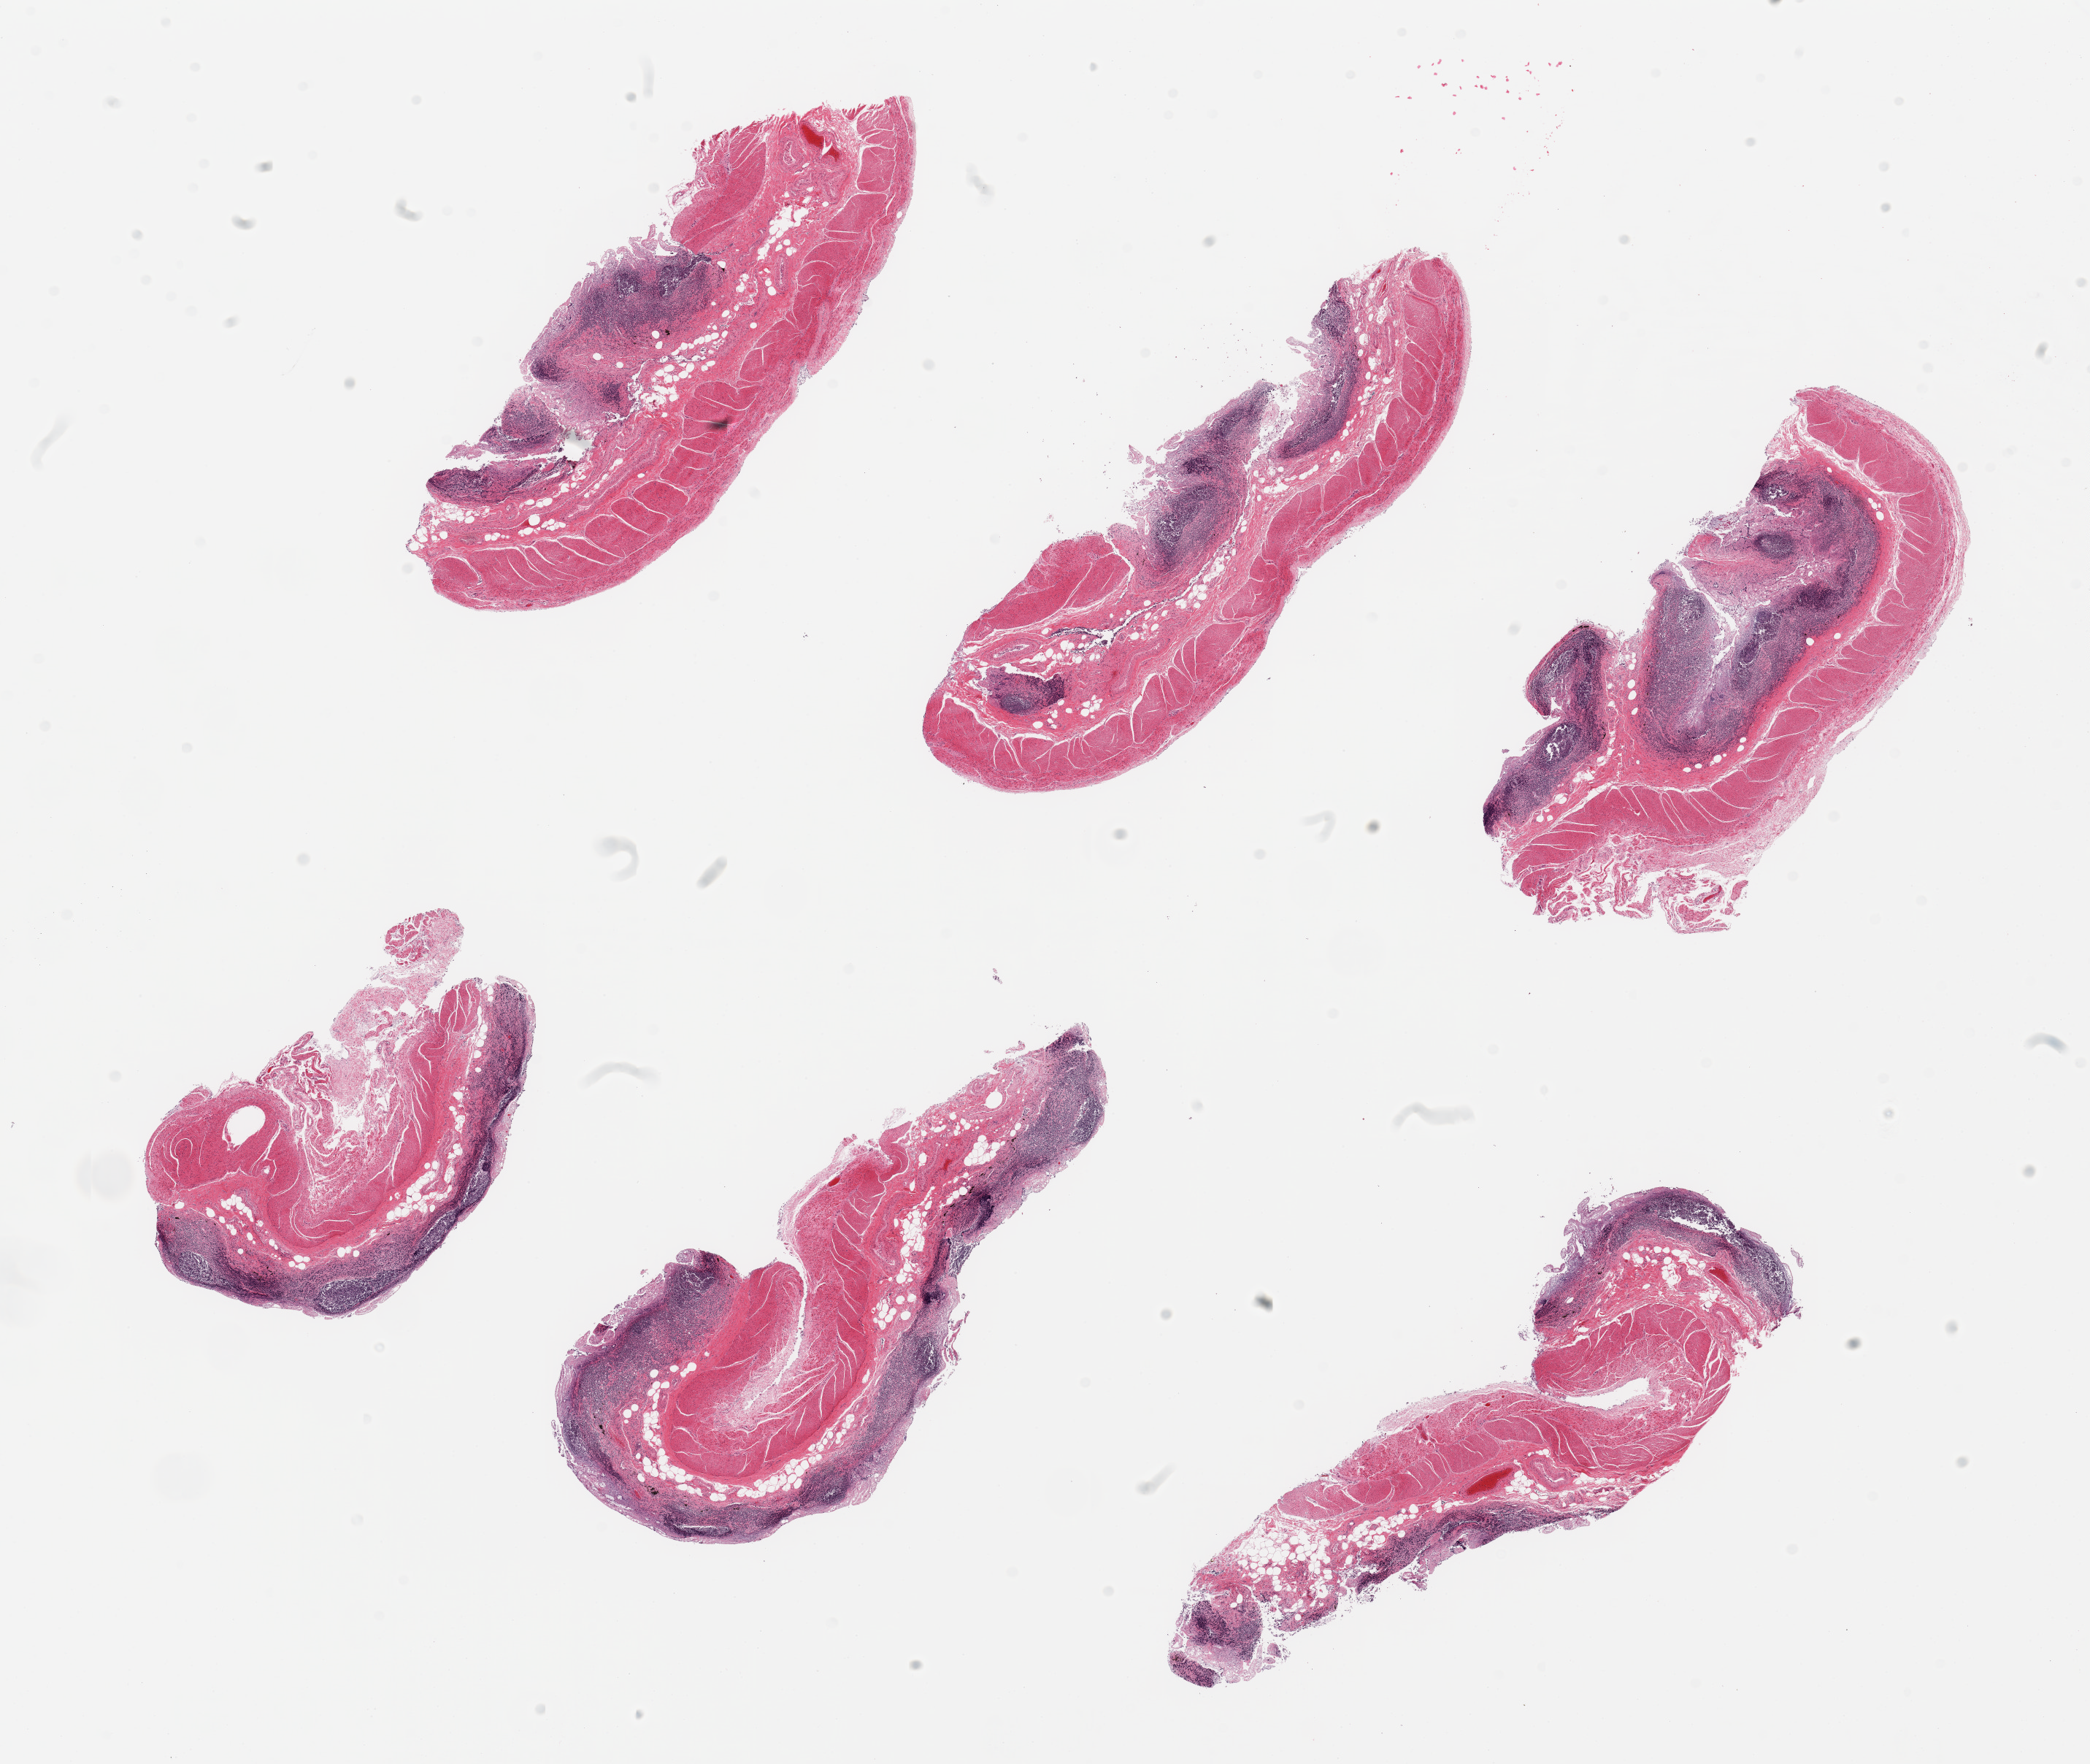
Whole-slide image, H&E stain — low-resolution overview of the scanned area, about 22.6 x 19.1 mm (acquisition: 20x scan); PAXgene-fixed, paraffin-embedded tissue; section of ileum (target tissue); donor tissue sample. Male donor.
Review note (as recorded): 6 pieces, glandular portion of mucosa completely autolyzed; residucal lympoid aggregates are ~25% total tissue.